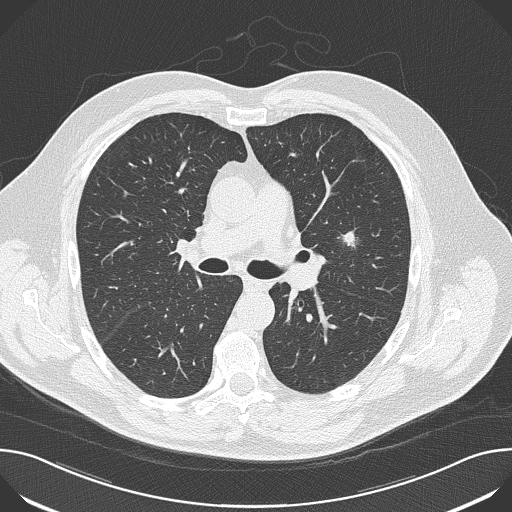
Chest CT (low-dose screening protocol), one axial image, baseline screening round, lung window (W 1500 / L -600 HU), slice 69 of 174 in the series. Male, age 65 years at enrolment. Former smoker at enrolment.
• Expert reader's lesion annotation, bounding box [x1, y1, x2, y2] px = [324, 223, 377, 269].
• The screening reader recorded 5 non-calcified nodules or masses ≥4 mm on this exam (left upper lobe, left upper lobe, left upper lobe, right upper lobe, right middle lobe); which of them this box marks is not recorded.
• Official screen result: positive, change unspecified: nodule(s) >= 4 mm or enlarging nodule(s), mass(es), or other non-specific abnormalities suspicious for lung cancer.